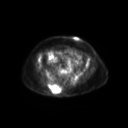
FDG PET of an extremity soft-tissue mass (from a PET/CT study), one axial slice; position 76 of 267 along the scan axis; 3.27 mm slice thickness; 128 × 128 image matrix, field of view 600 × 600 mm. Patient: female, 60 years. Case-level facts recorded for this patient, not image findings: histological type: spindle cell suggestive of myxofibrosarcoma; grade: intermediate; site of the primary tumour: right buttock.
Annotated regions visible in this slice (expert contour drawn on MRI and transferred to this co-registered scan by the dataset authors):
- gross tumour volume (mass): bounding box <42,83,63,94> (left, top, right, bottom; pixels)